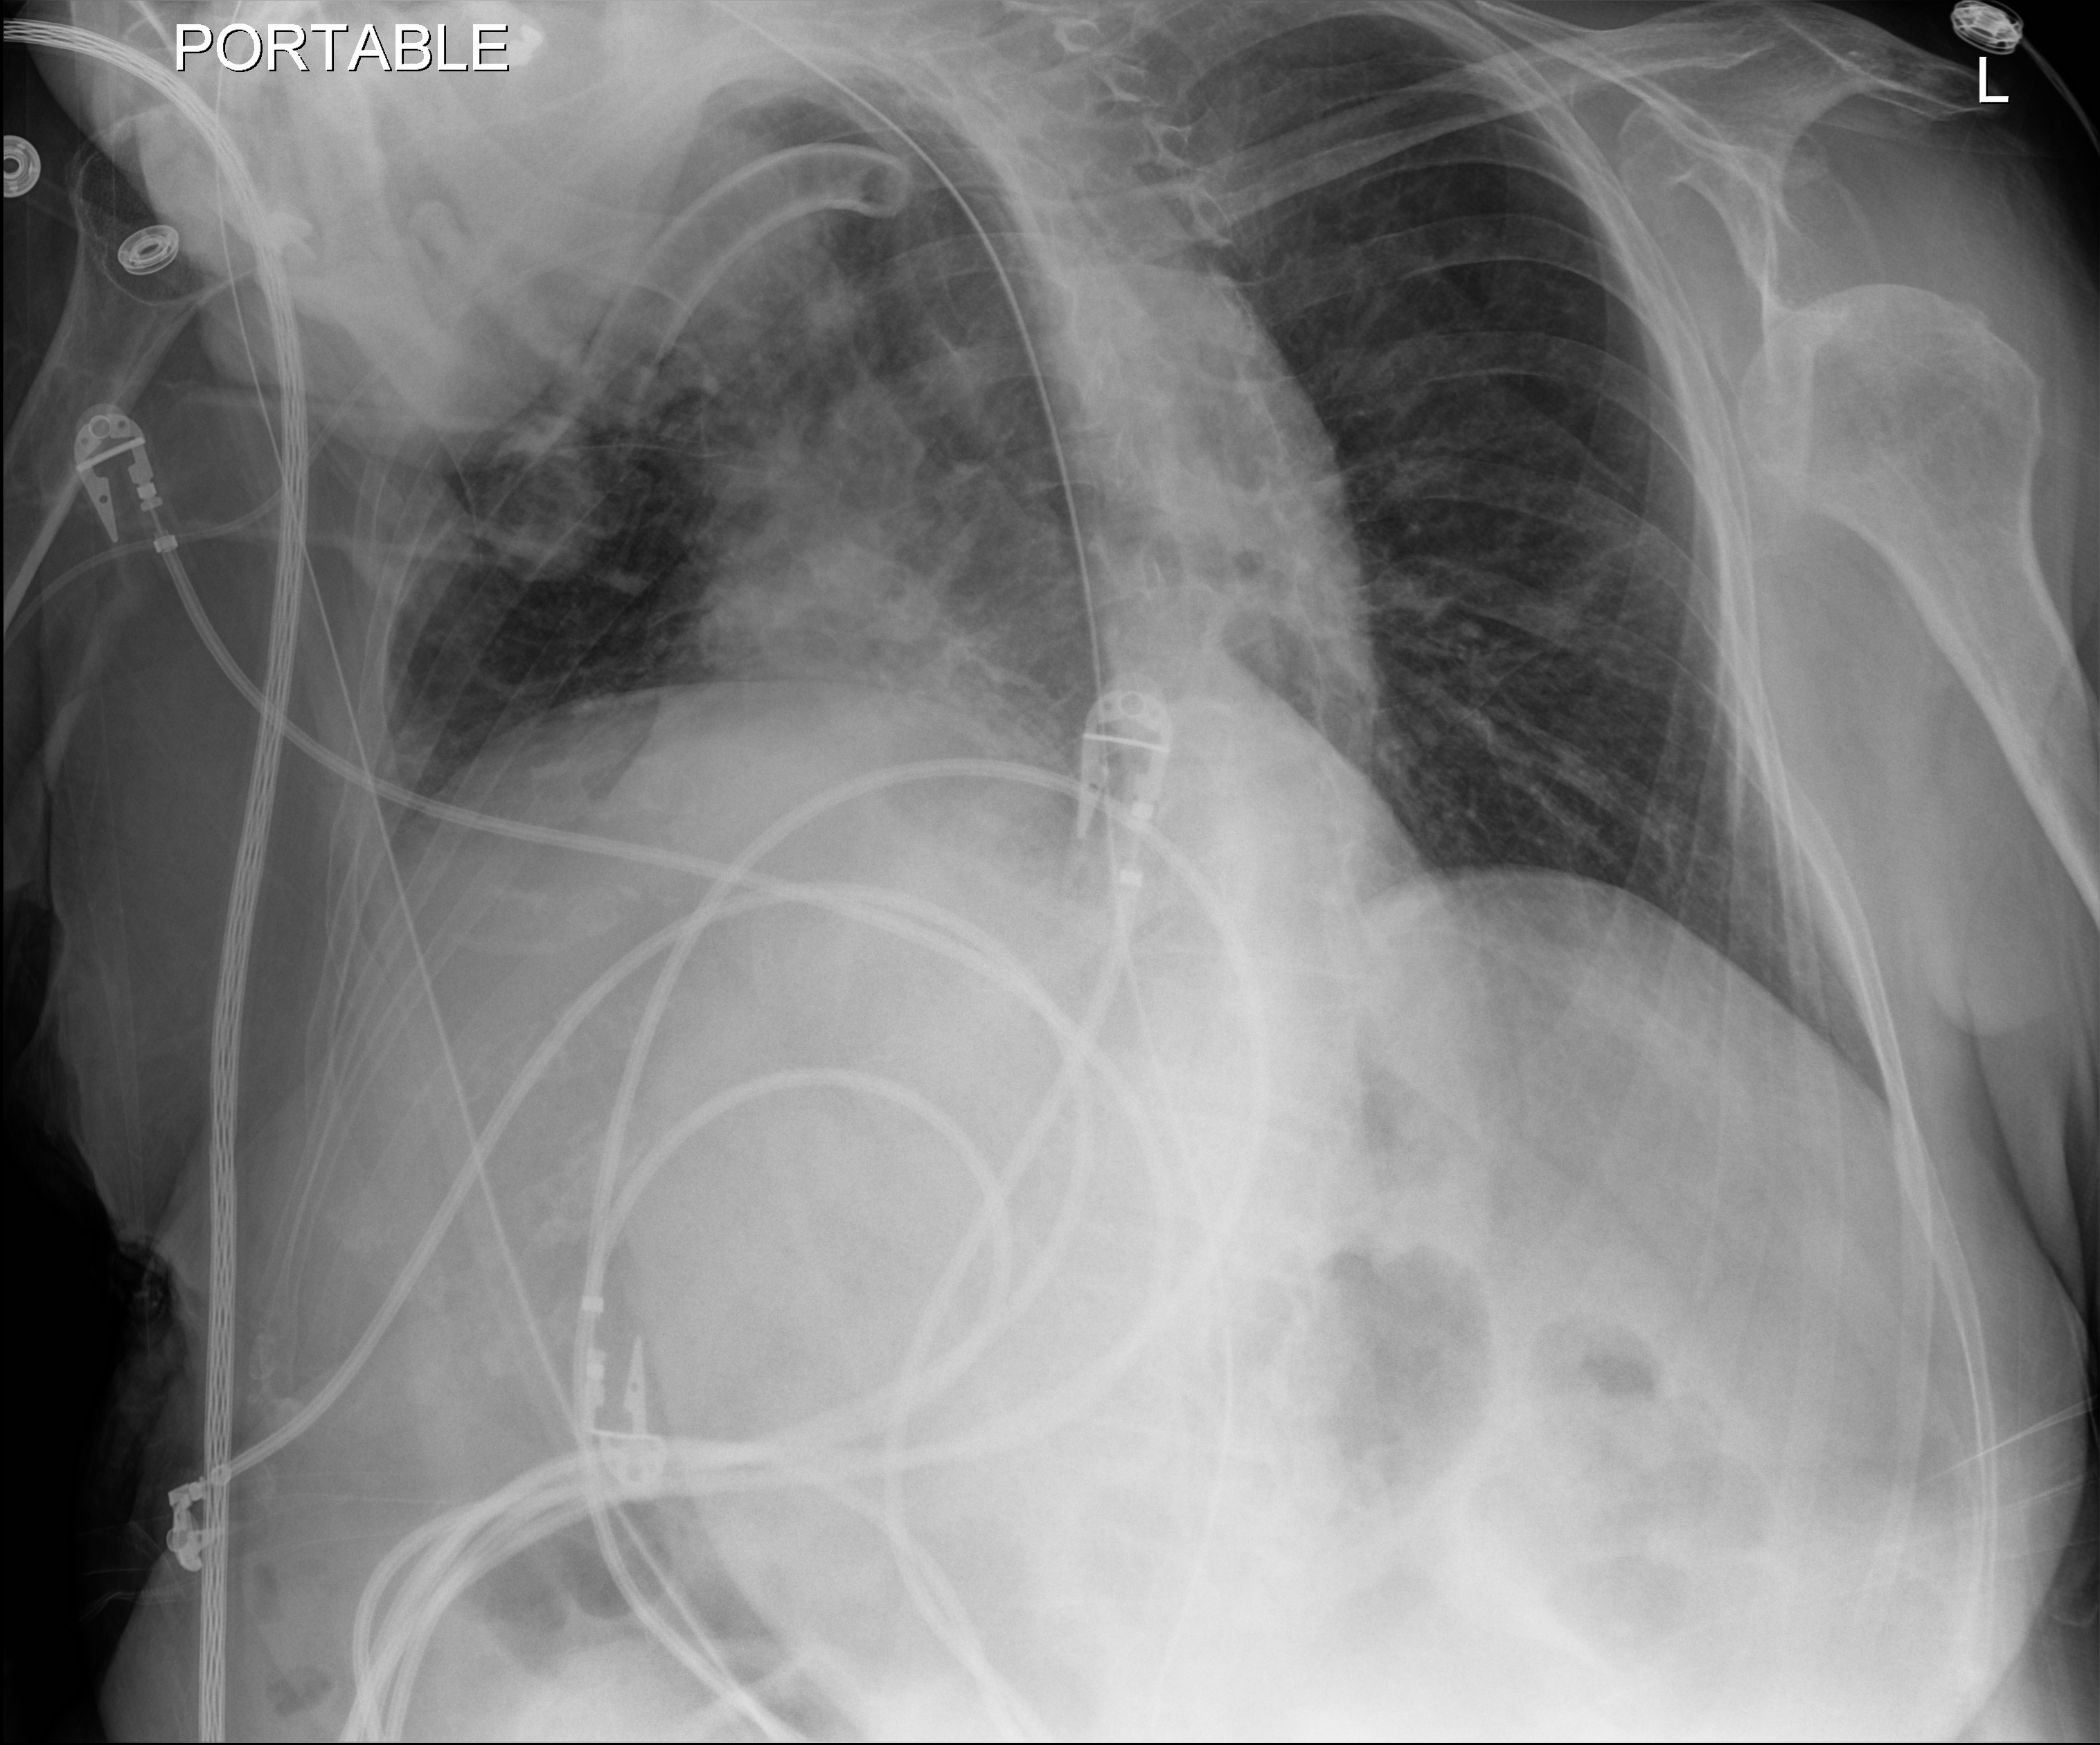
Chest radiograph, anteroposterior (AP) projection. Female patient hospitalised with COVID-19, age 75–90 years.
Admission-level facts for this patient (not findings on this image; timing relative to this image not recorded): hypertension (admission record): yes; admitted to intensive care during this hospital stay: yes.